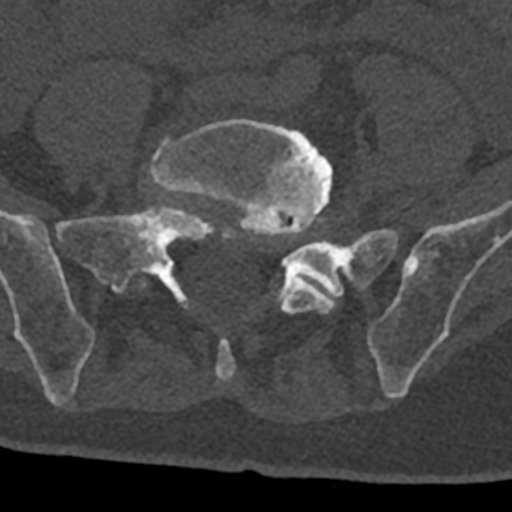
CT including the spine, one axial slice; position 175 of 797 along the scan axis; 120 kVp; bone window (W 1800 / L 400 HU); 512 × 512 image matrix, field of view 160 × 160 mm. Male patient, age 74 years. Case-level facts recorded for this patient, not image findings: primary cancer: renal; vertebrae with lytic lesions (as recorded): T10, L1, L2, L3, L4, L5.
Structures marked on this image (semi-automatic segmentation, software-assisted and operator-edited):
- L5 vertebra: bounding box (x1, y1, x2, y2) in pixels: (139, 118, 349, 381)